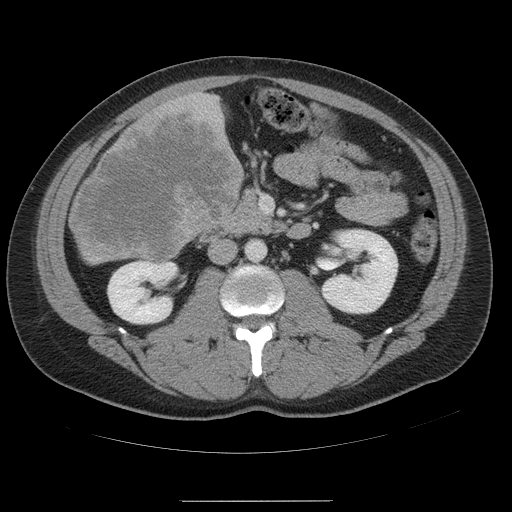
Contrast-enhanced abdominal CT, one axial slice. Position 18 of 54 along the scan axis. Intravenous contrast given. Soft-tissue window (W 400 / L 40 HU). 5 mm slice thickness. 512 × 512 image matrix, field of view 436 × 436 mm. Male patient, age 40 years. From the clinical record (not read from this slice): diagnosis: colorectal cancer liver metastases, imaged before liver resection.
Structures marked on this image (expert manual segmentation):
- liver: bounding box [x1, y1, x2, y2] px = [70, 93, 244, 264]
- liver metastasis: [71, 107, 243, 261]